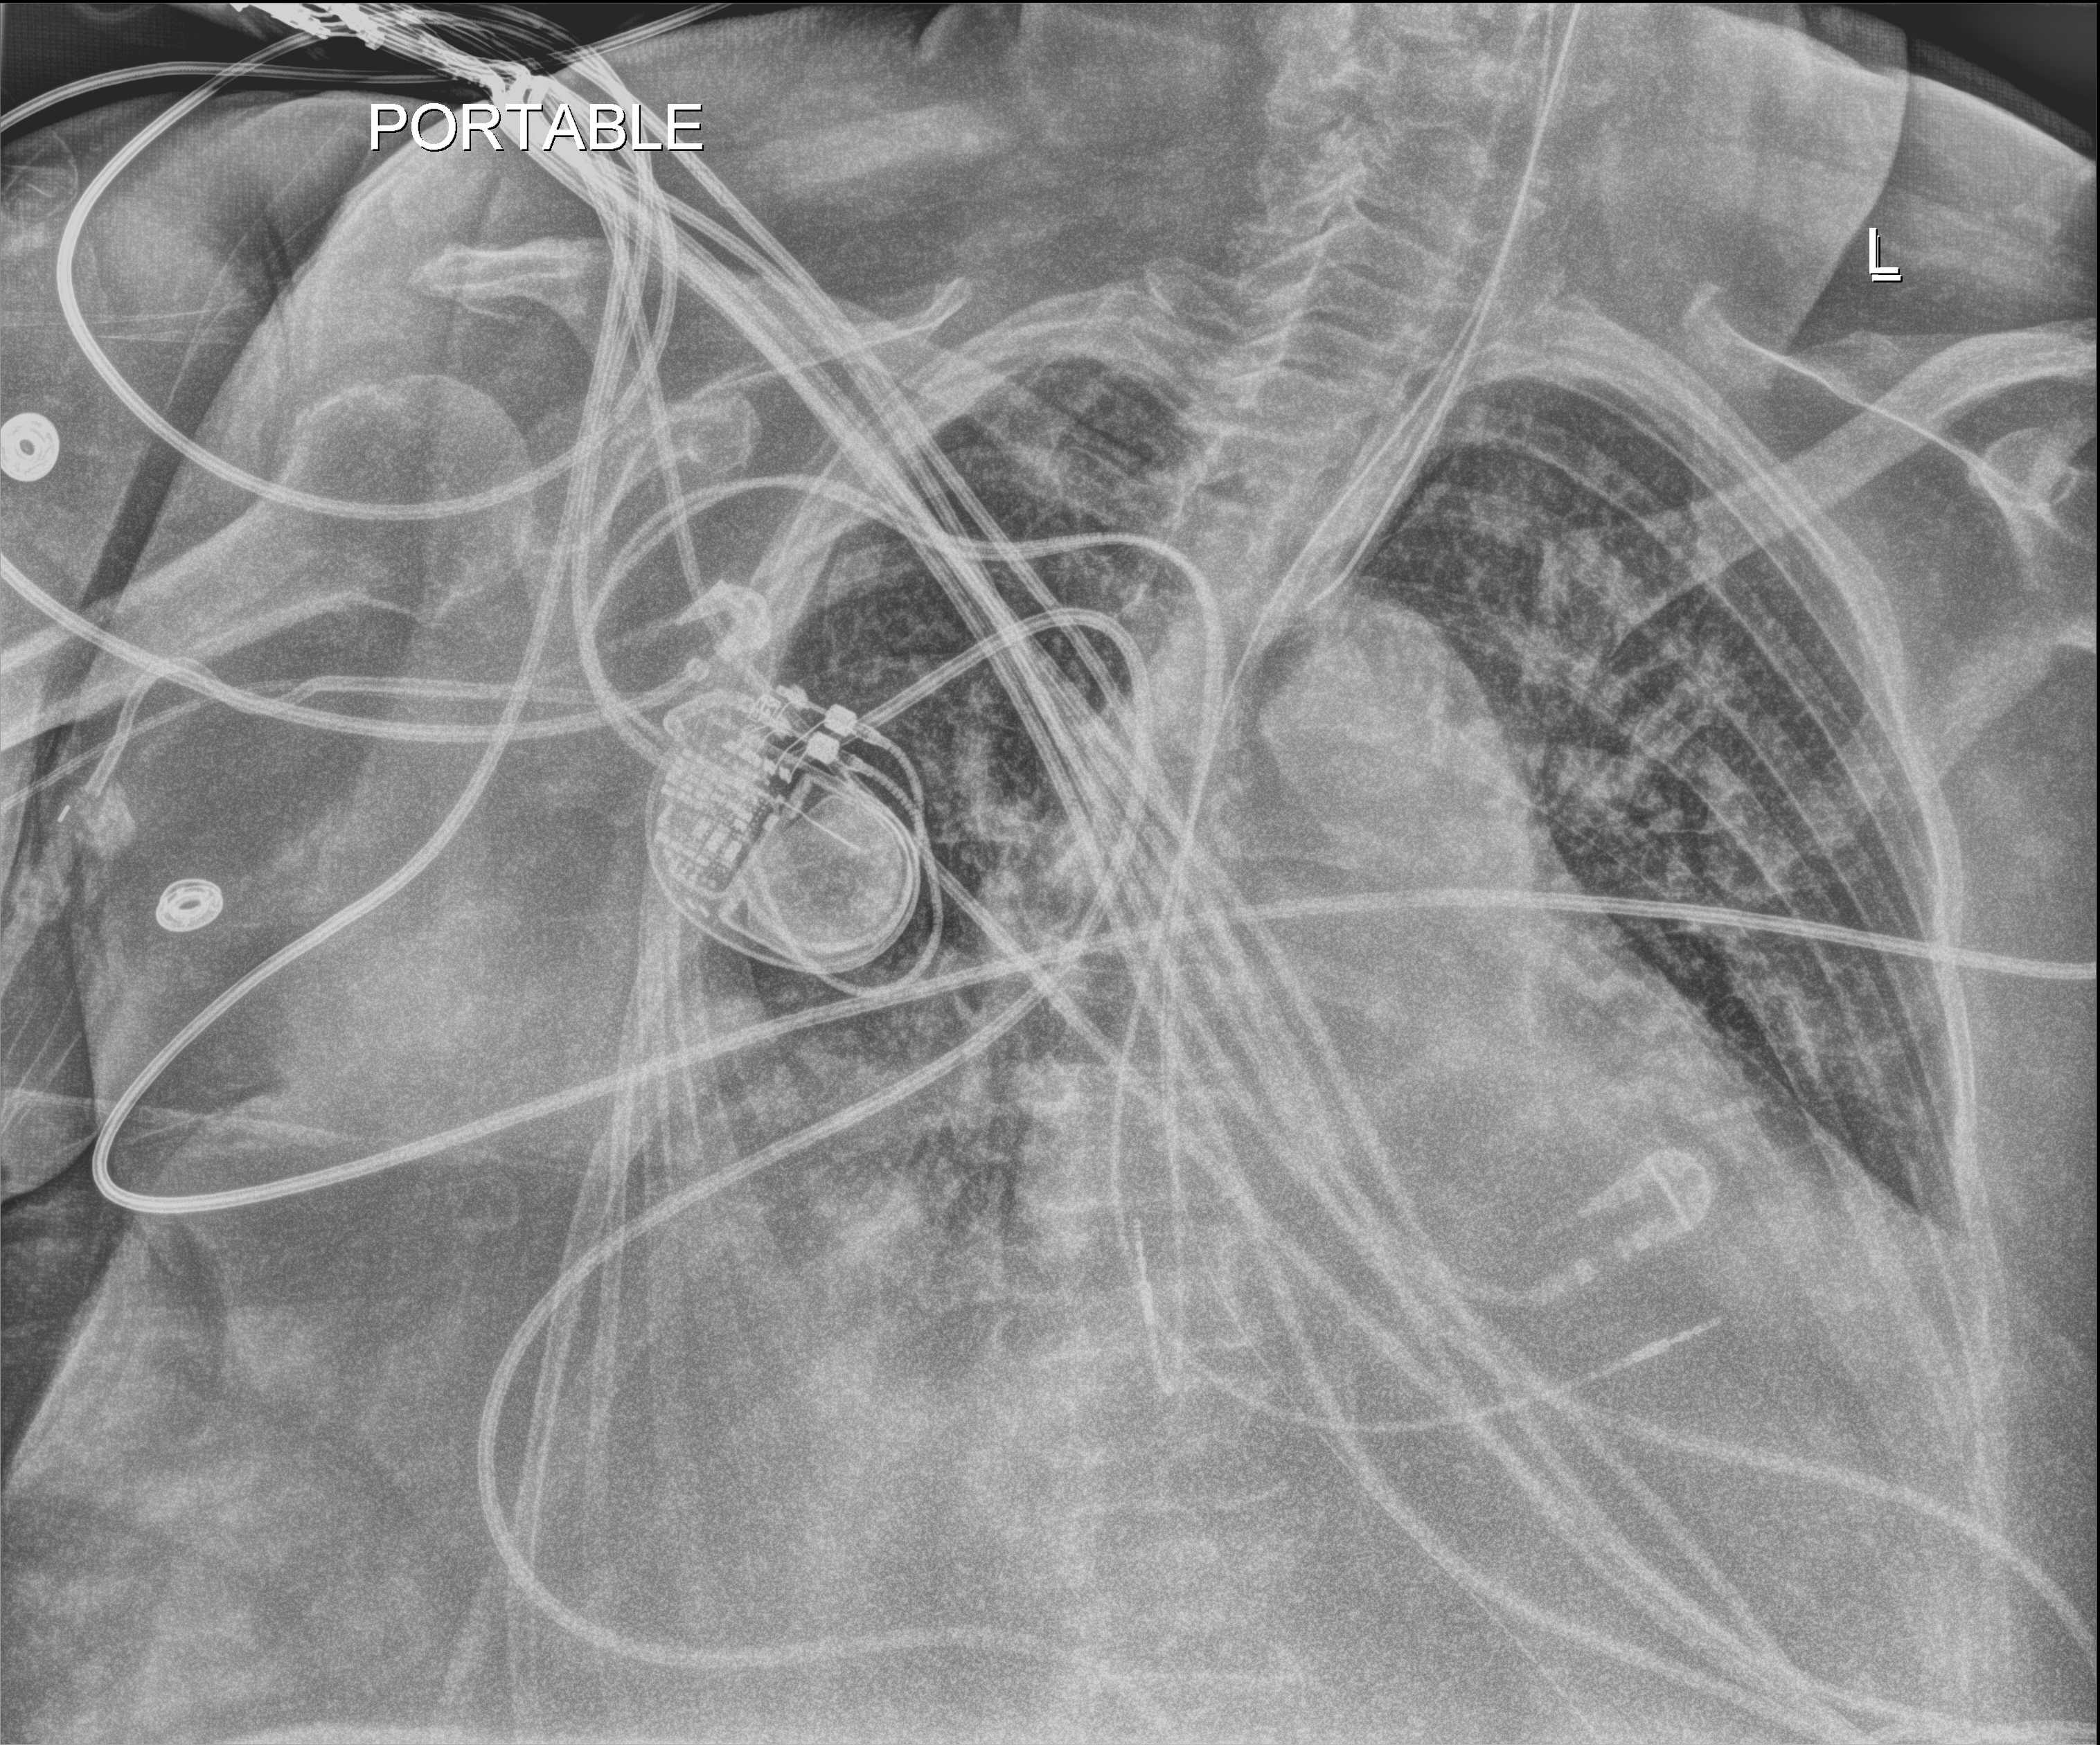
Chest X-ray (portable), anteroposterior (AP) projection. Female patient hospitalised with COVID-19, age 75–90 years.
Hospital-stay facts (about this admission, not read from this image; timing relative to this image not recorded): length of hospital stay: 21 days; hypertension (admission record): yes.